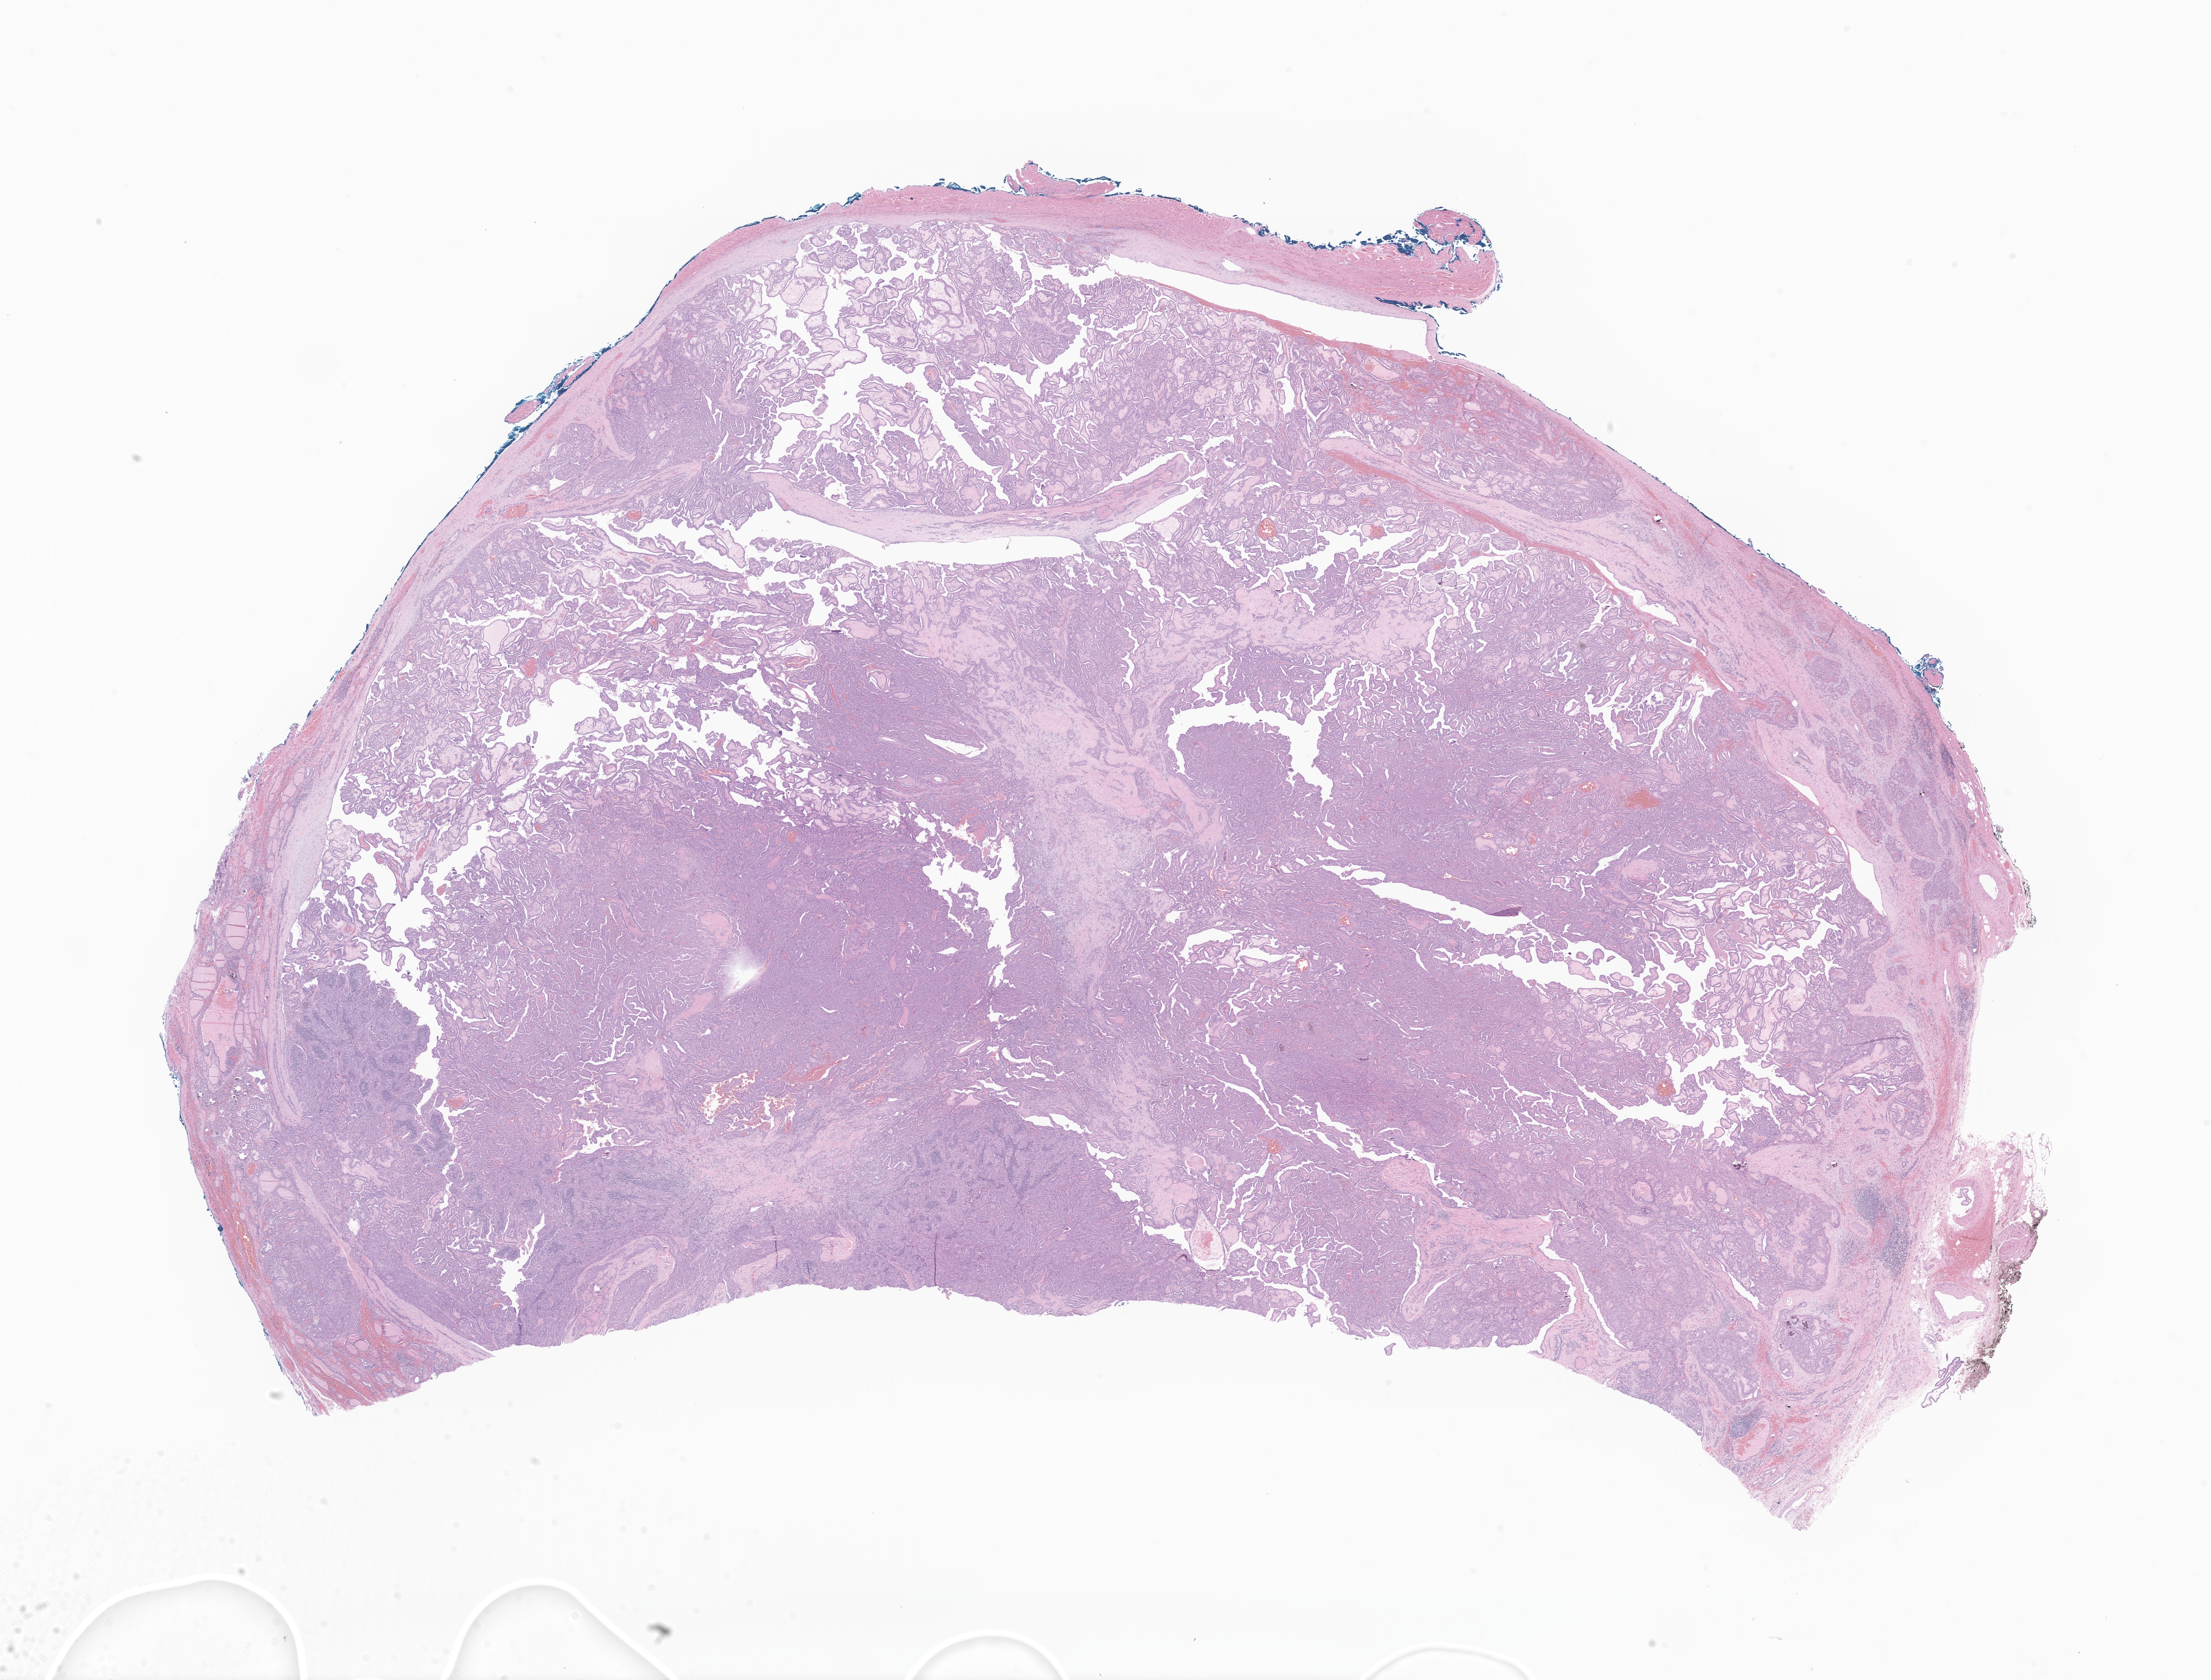
Digitized haematoxylin and eosin-stained section of tumor tissue from the thyroid, low-resolution overview of the scanned area, about 25.8 x 19.6 mm. FFPE section. Patient female; age 181 months.
Recorded diagnosis: Papillary carcinoma, NOS.